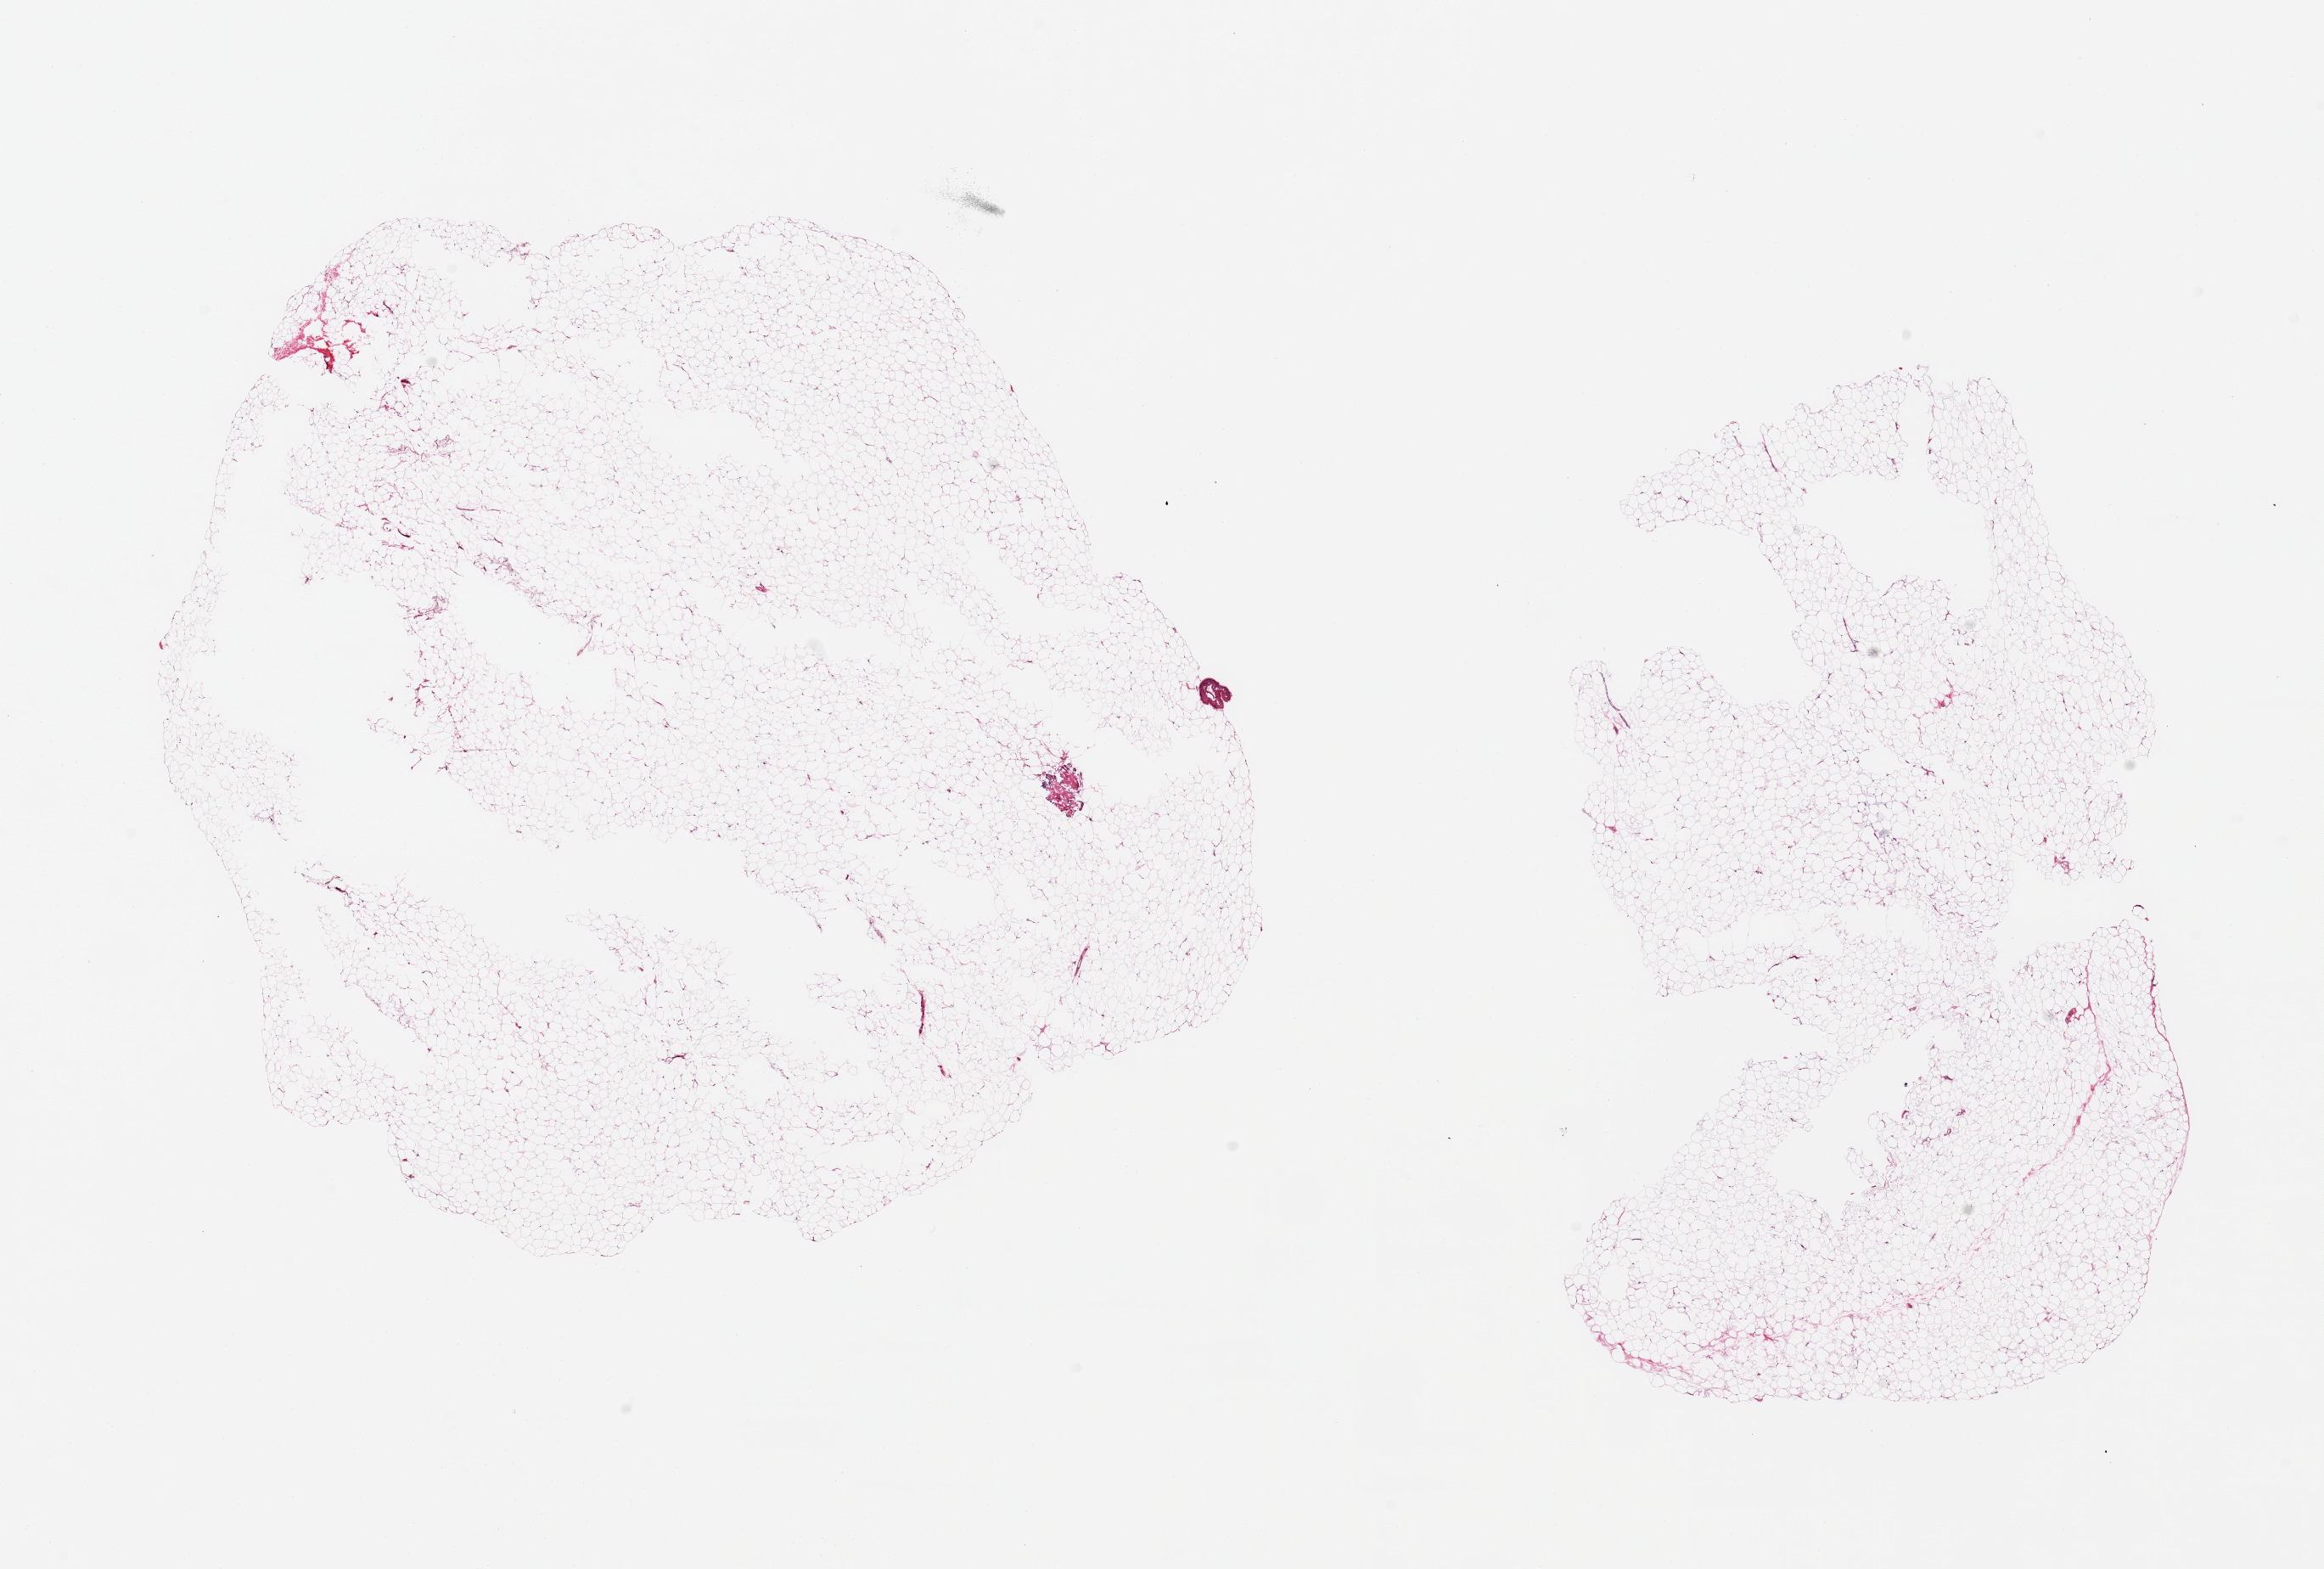
Digitized H&E-stained section — low-resolution overview of the scanned area, about 21.7 x 14.6 mm (from a 20x scan). PAXgene-fixed, paraffin-embedded tissue. Section of breast (target tissue). Donor tissue sample. Donor sex: female.
Pathologist's review note for this sample: 2 pieces, adipose elements only.